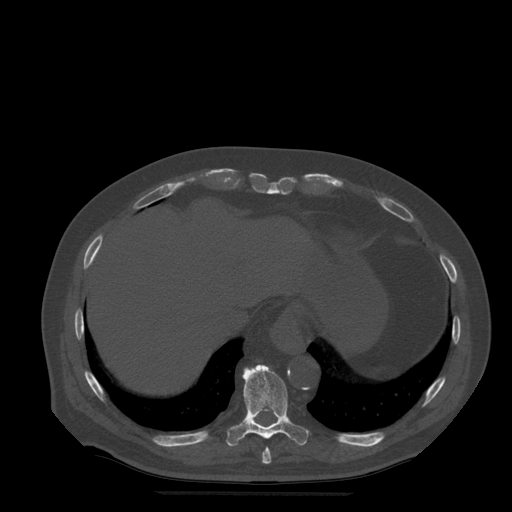
CT including the spine, one axial slice. Slice 269 of 522 in the series (ordered by position). Bone window (W 1800 / L 400 HU). 512 × 512 image matrix, field of view 420 × 420 mm. Patient age 72 years. Case-level facts recorded for this patient, not image findings: primary cancer: prostate.
Structures marked on this image (semi-automatically segmented with operator editing):
- T10 vertebra: box from (x=227, y=365) to (x=310, y=447) px
- T9 vertebra: (x=262, y=448)–(x=272, y=464)